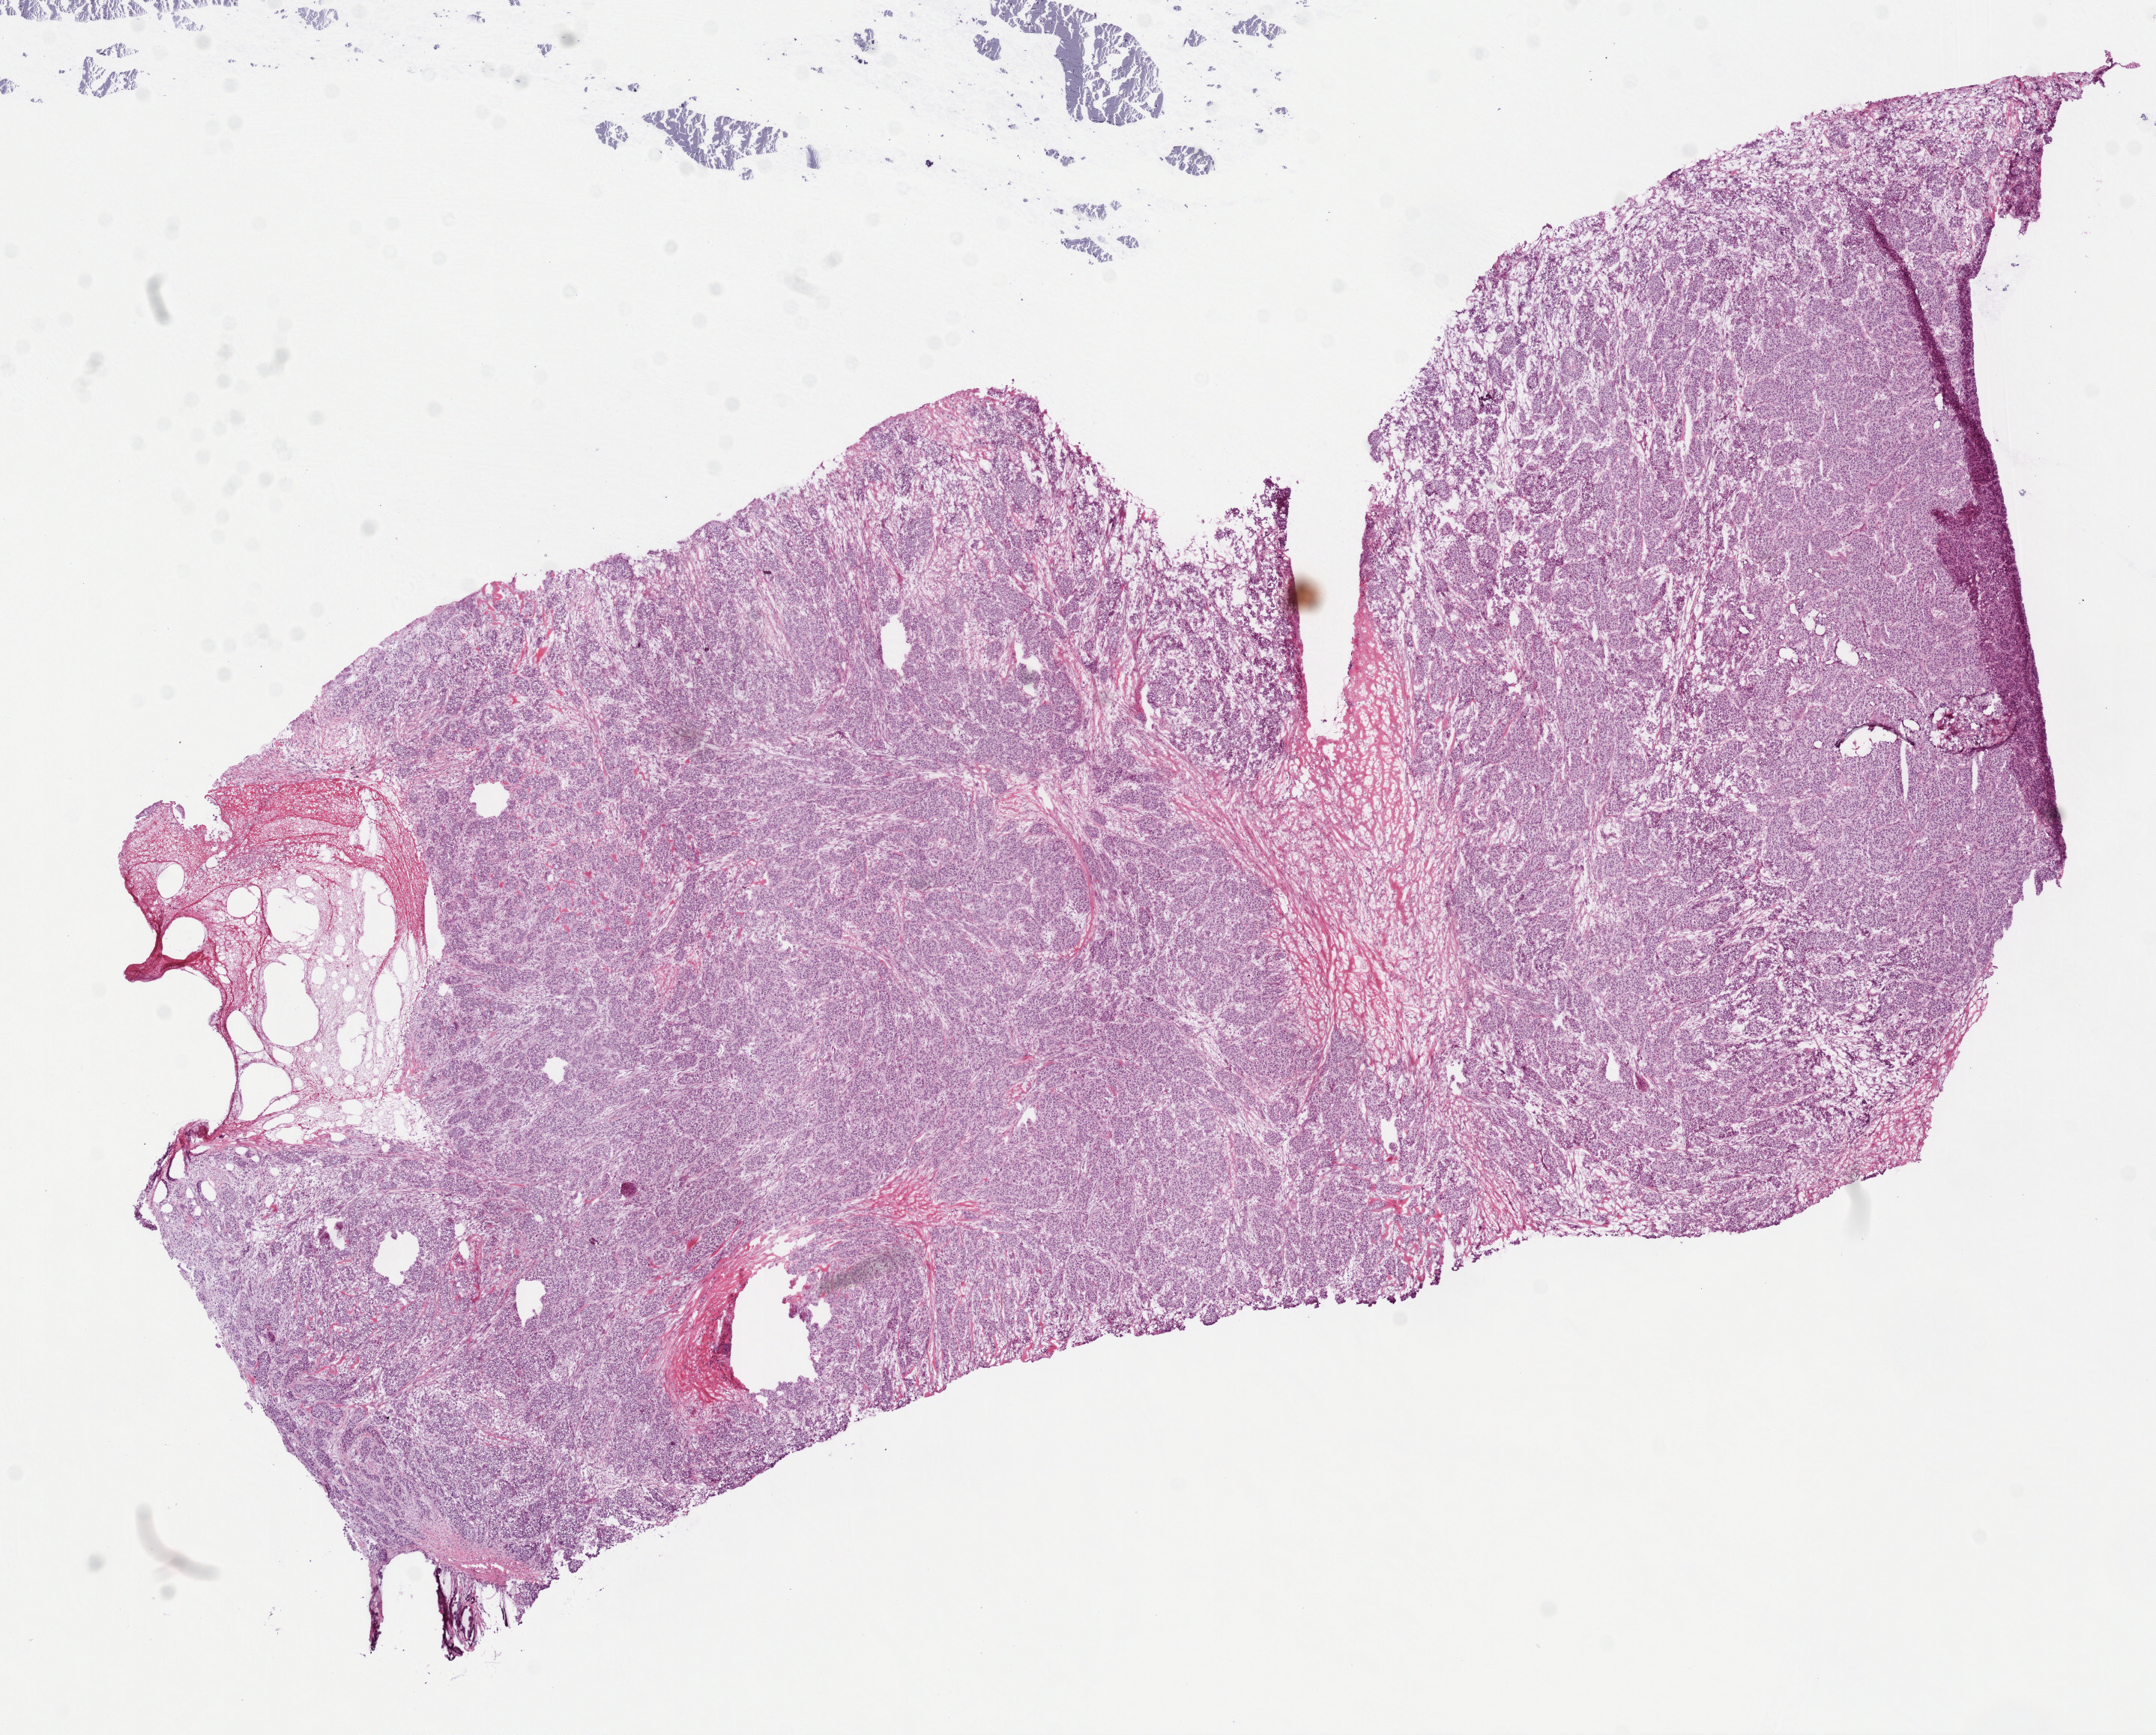
Digitized H&E-stained tissue section (whole slide) — low-resolution overview of the scanned area, about 11.6 x 9.3 mm (from a 40x scan). Frozen section from the top of the tissue portion. Breast, primary tumour sample. Male, age 58 years at initial diagnosis. Composition of this section per pathologist review: tumour cells 70%, tumour nuclei 70%.
Diagnosis: Infiltrating duct carcinoma, NOS.